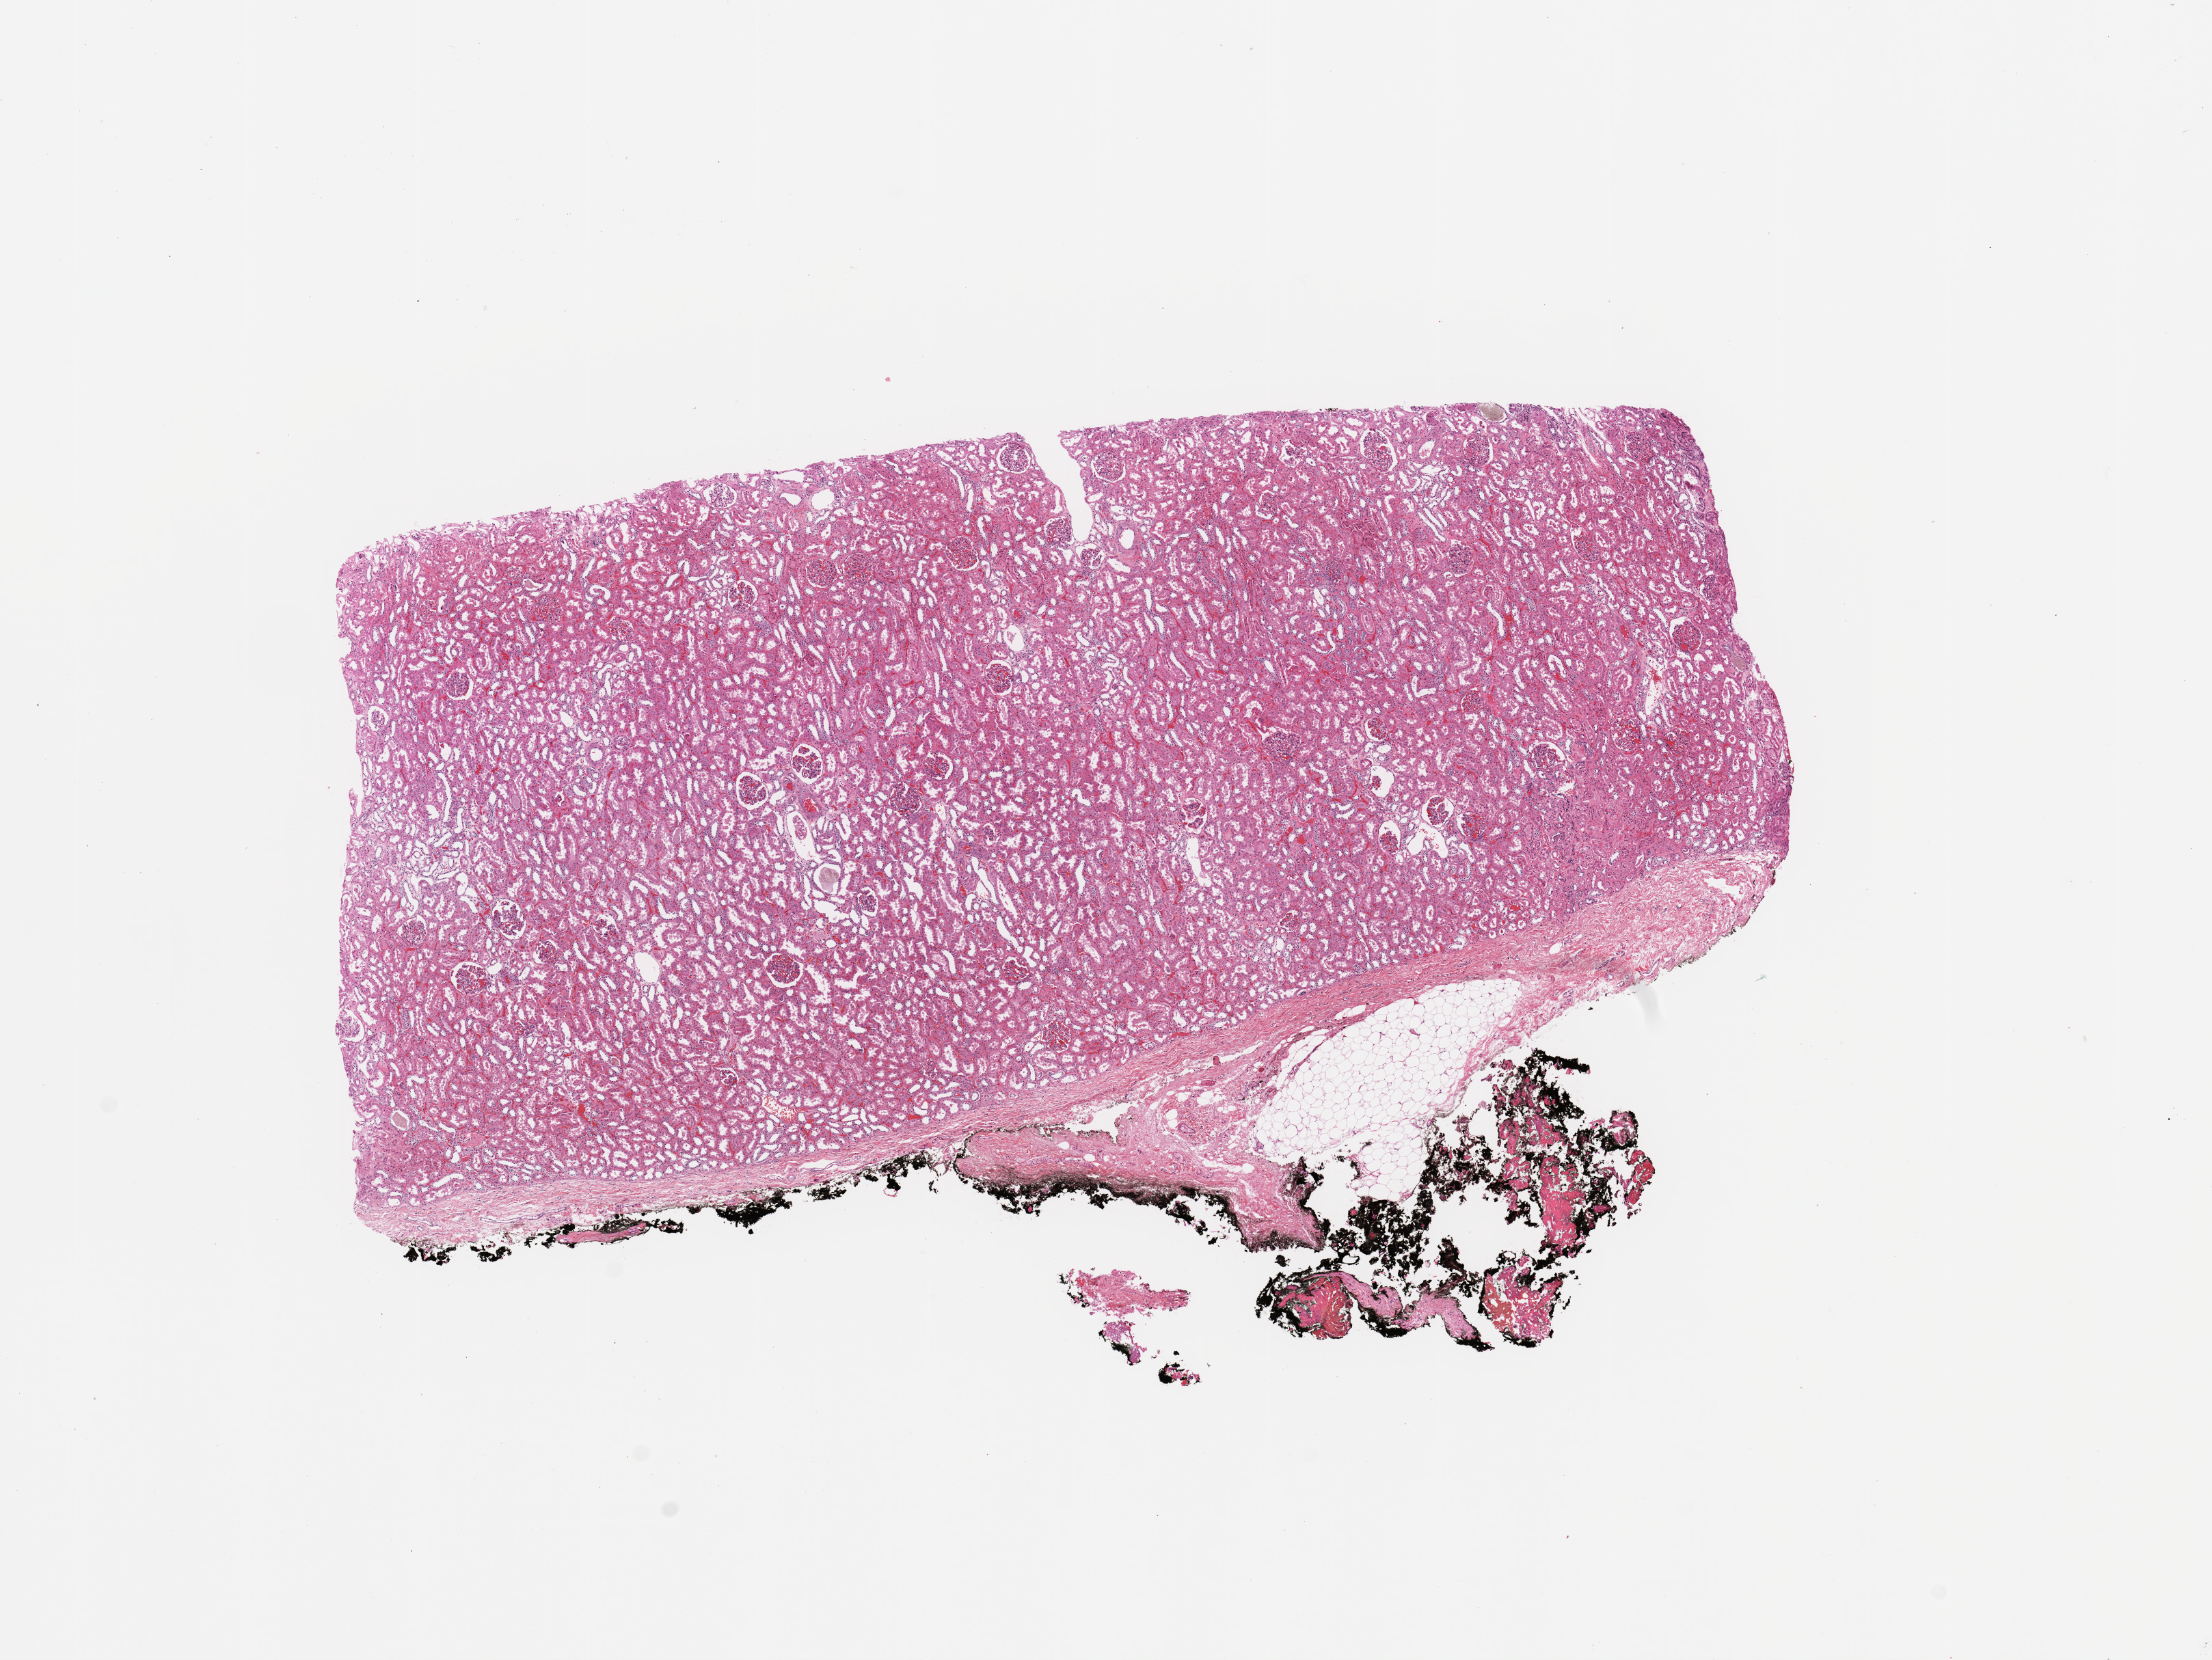
H&E whole-slide image, shown as a low-resolution overview of the whole scanned area (about 12.8 x 9.6 mm, from a 20x scan), normal (non-tumour) tissue sample, sampled site: kidney. 43-year-old male patient.
This section: normal (non-tumour) tissue from the same patient. Patient diagnosis: Renal cell carcinoma, NOS.